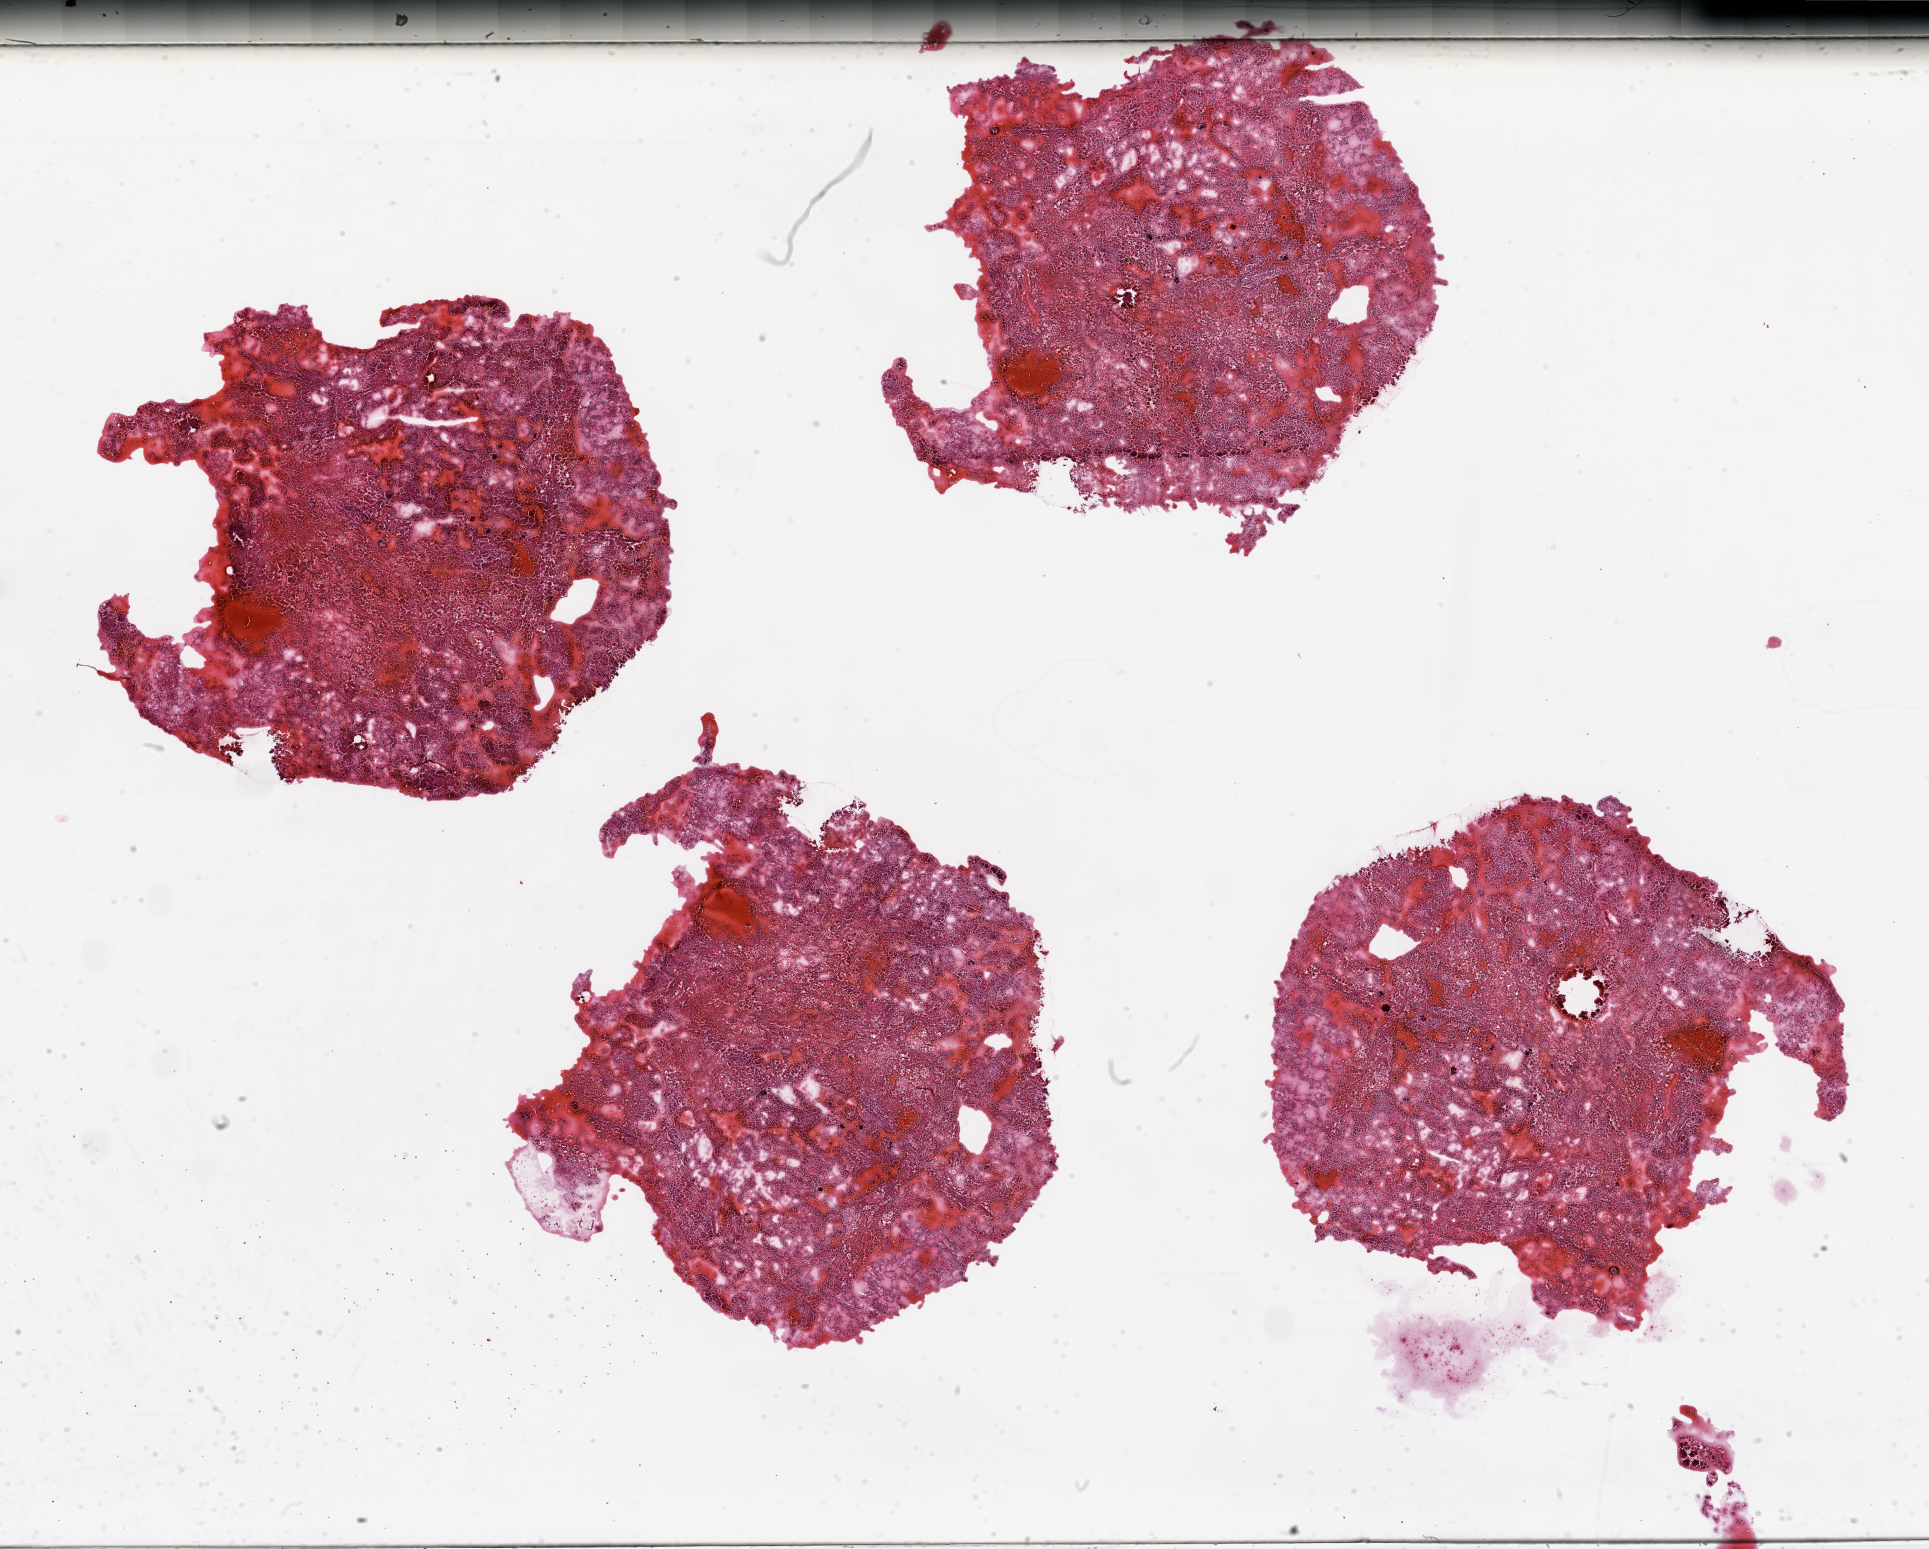
Digitized Hematoxylin and eosin (H&E) stained tissue section (whole slide), a low-resolution overview of the entire scanned area, about 30.5 x 24.5 mm, kidney, tumour tissue. 31-year-old female patient.
Histologic diagnosis: Renal cell carcinoma, NOS.